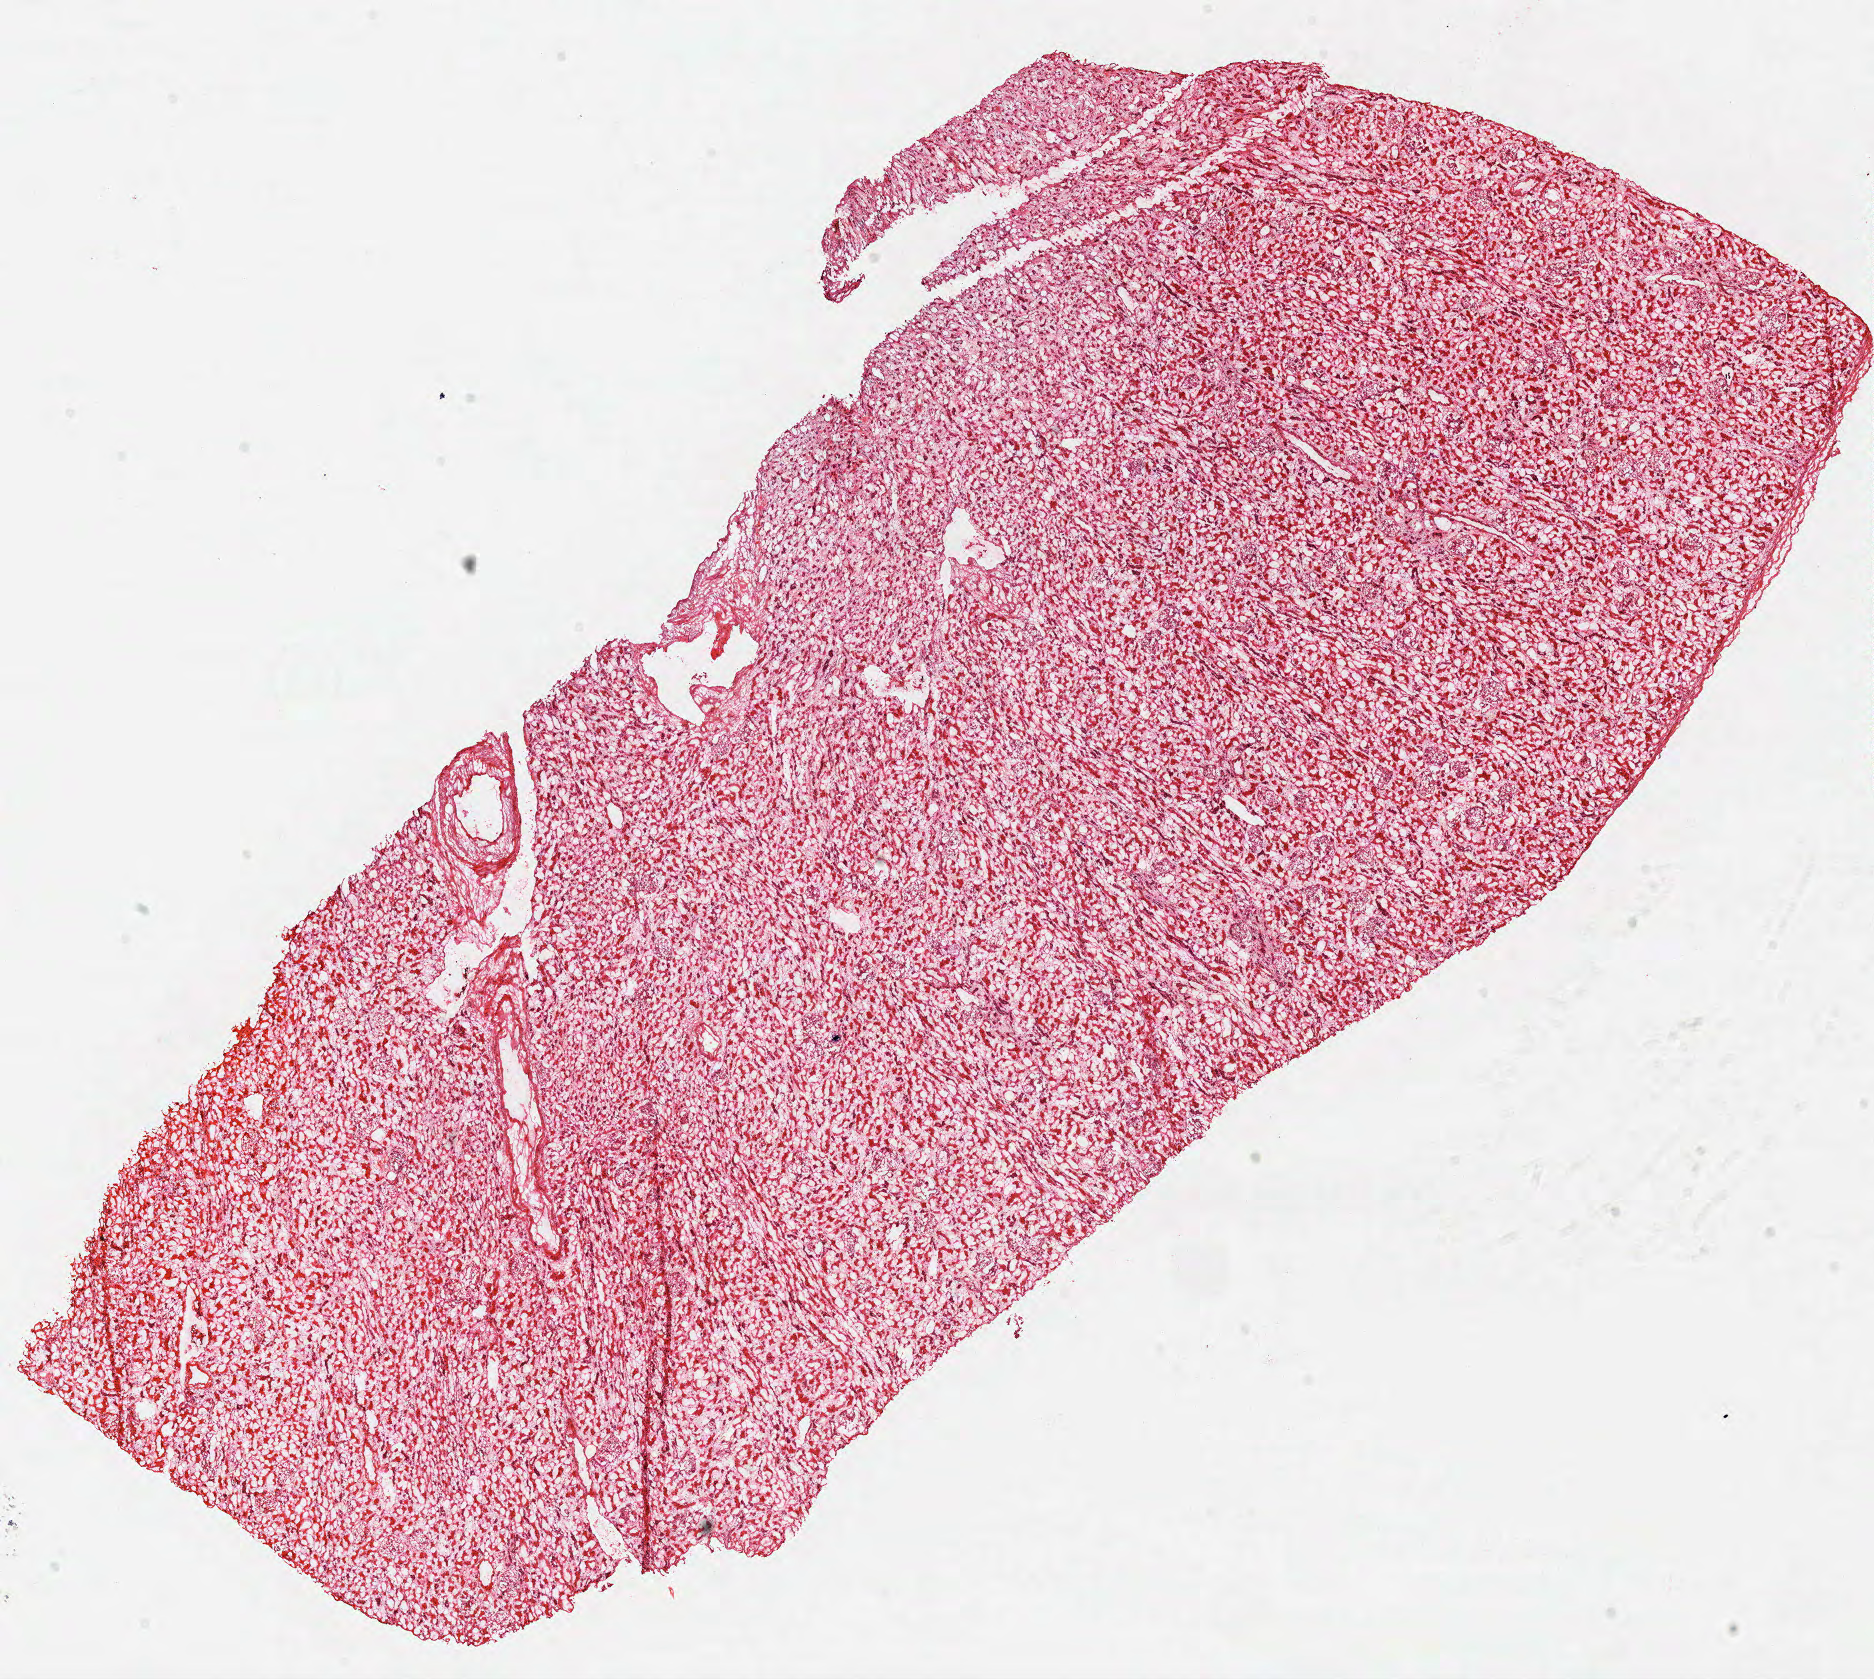
H&E whole-slide image — whole scanned area (about 14.8 x 13.2 mm) shown as a low-resolution overview; frozen section; sample: solid tissue normal (non-tumour tissue), kidney. Male patient; age at initial diagnosis 61 years.
- this section: solid tissue normal (non-tumour) sample from the same patient
- patient diagnosis: Clear cell adenocarcinoma, NOS